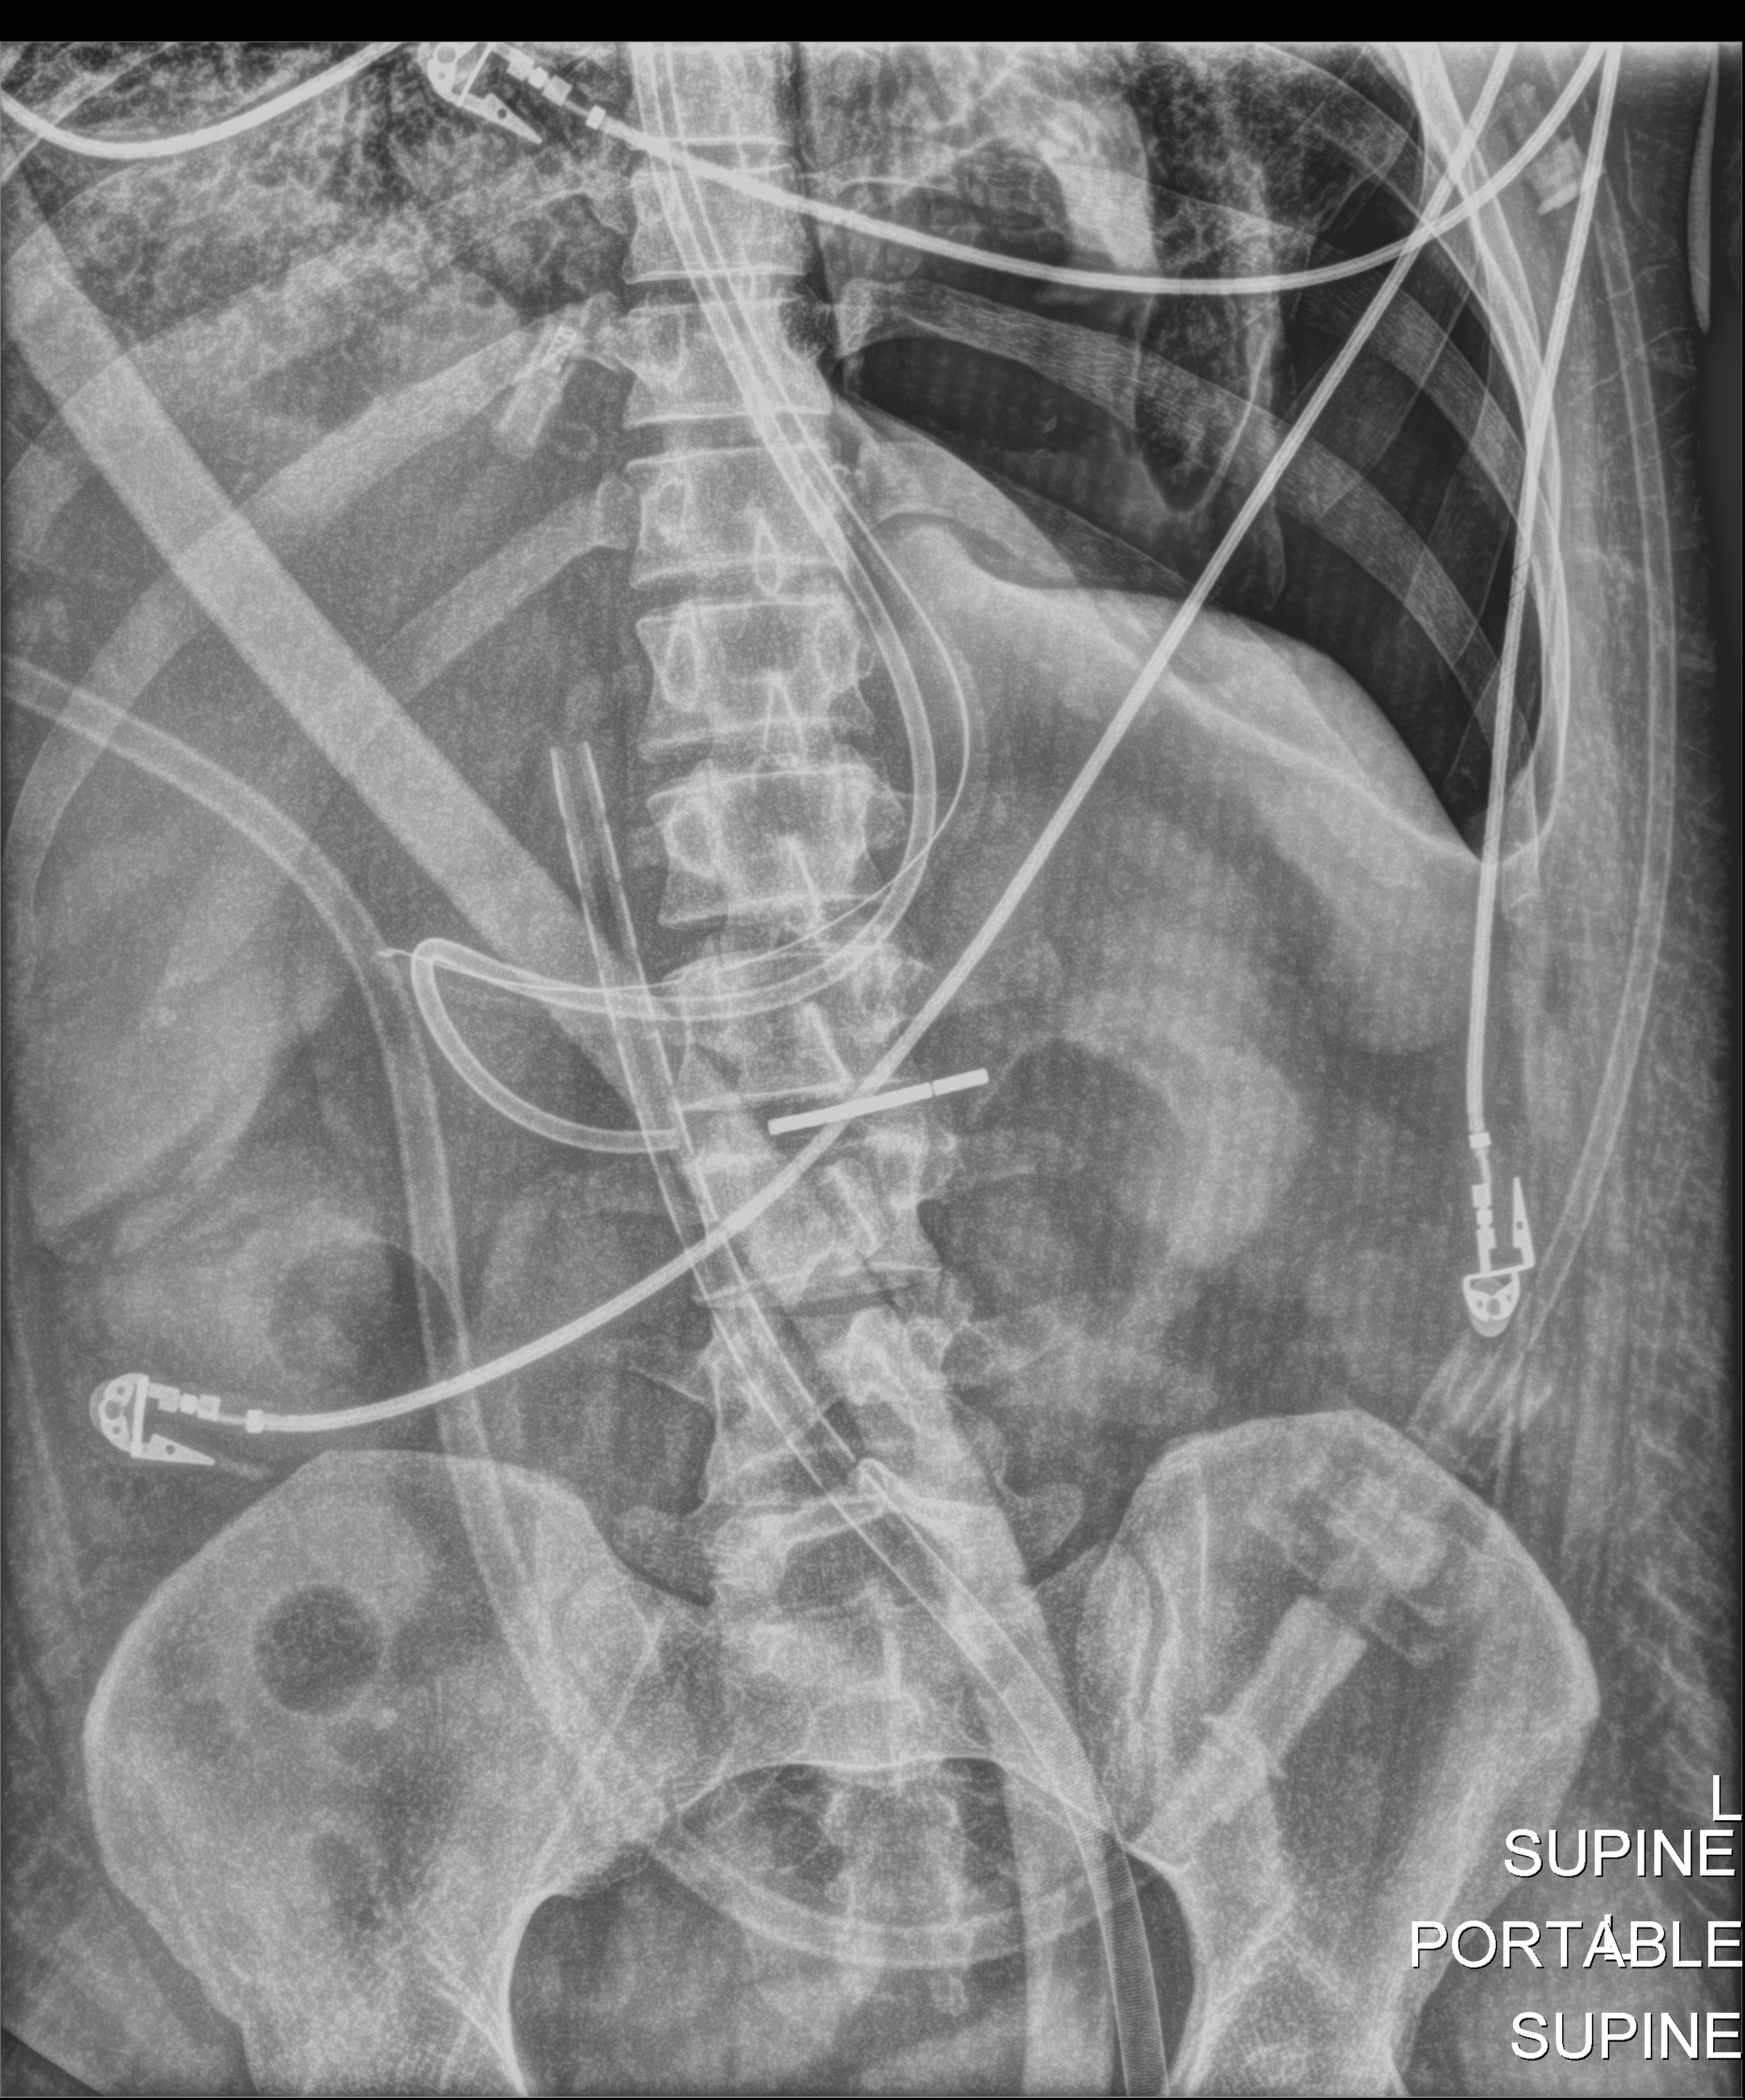
Portable abdomen radiograph, anteroposterior (AP) projection. Patient hospitalised with COVID-19, aged 18–59 years.
From the hospital-stay record, not from the radiograph (when in the stay this image was taken is not recorded):
- admitted to intensive care during this hospital stay: yes
- other chronic lung disease (admission record): no
- mechanically ventilated during this hospital stay: yes